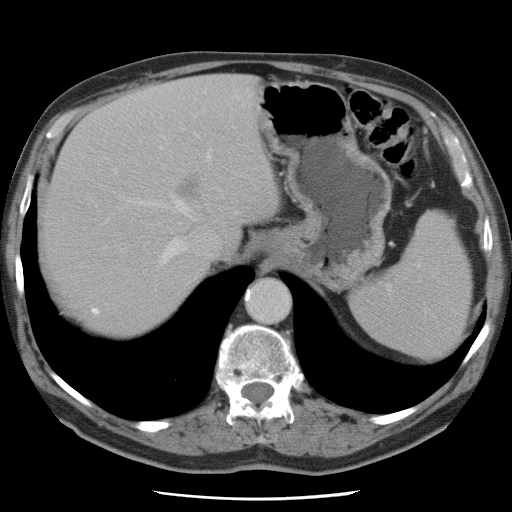
Contrast-enhanced abdominal CT, one axial slice. Position 60 of 78 along the scan axis. 120 kVp. Intravenous contrast given. Soft-tissue window (W 400 / L 40 HU). 5 mm slice thickness. 512 × 512 image matrix, field of view 337 × 337 mm. Male patient, age 75 years. Case-level facts recorded for this patient, not image findings: diagnosis: colorectal cancer liver metastases, imaged before liver resection; multiple liver metastases: yes; largest metastasis: 2.4 cm; chemotherapy before resection: yes.
Annotated regions visible in this slice (expert manual segmentation):
- hepatic veins: bounding box <120,96,236,265> (left, top, right, bottom; pixels)
- liver: <42,77,274,333>
- planned liver remnant (the part of the liver to remain after resection): <42,134,205,333>
- portal vein (with intrahepatic branches): <113,170,116,172>
- liver metastasis: <92,308,100,315>
- liver metastasis: <177,179,199,199>